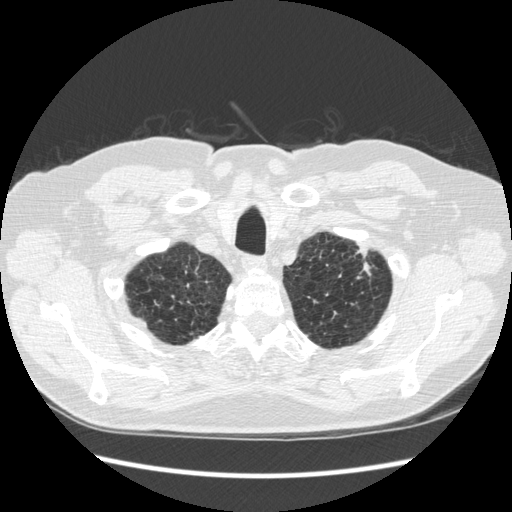
Low-dose screening chest CT, one axial slice; position 241 of 267 along the scan axis; reconstruction kernel STANDARD; 120 kVp; lung window (W 1500 / L -600 HU); 1.25 mm slice thickness; 512 × 512 image matrix, field of view 360 × 360 mm.
Outlined on this slice (outlined manually by an expert reader):
- lesion 1 (tumor, upper lobe of left lung): bounding box [x1, y1, x2, y2] px = [357, 253, 371, 278]